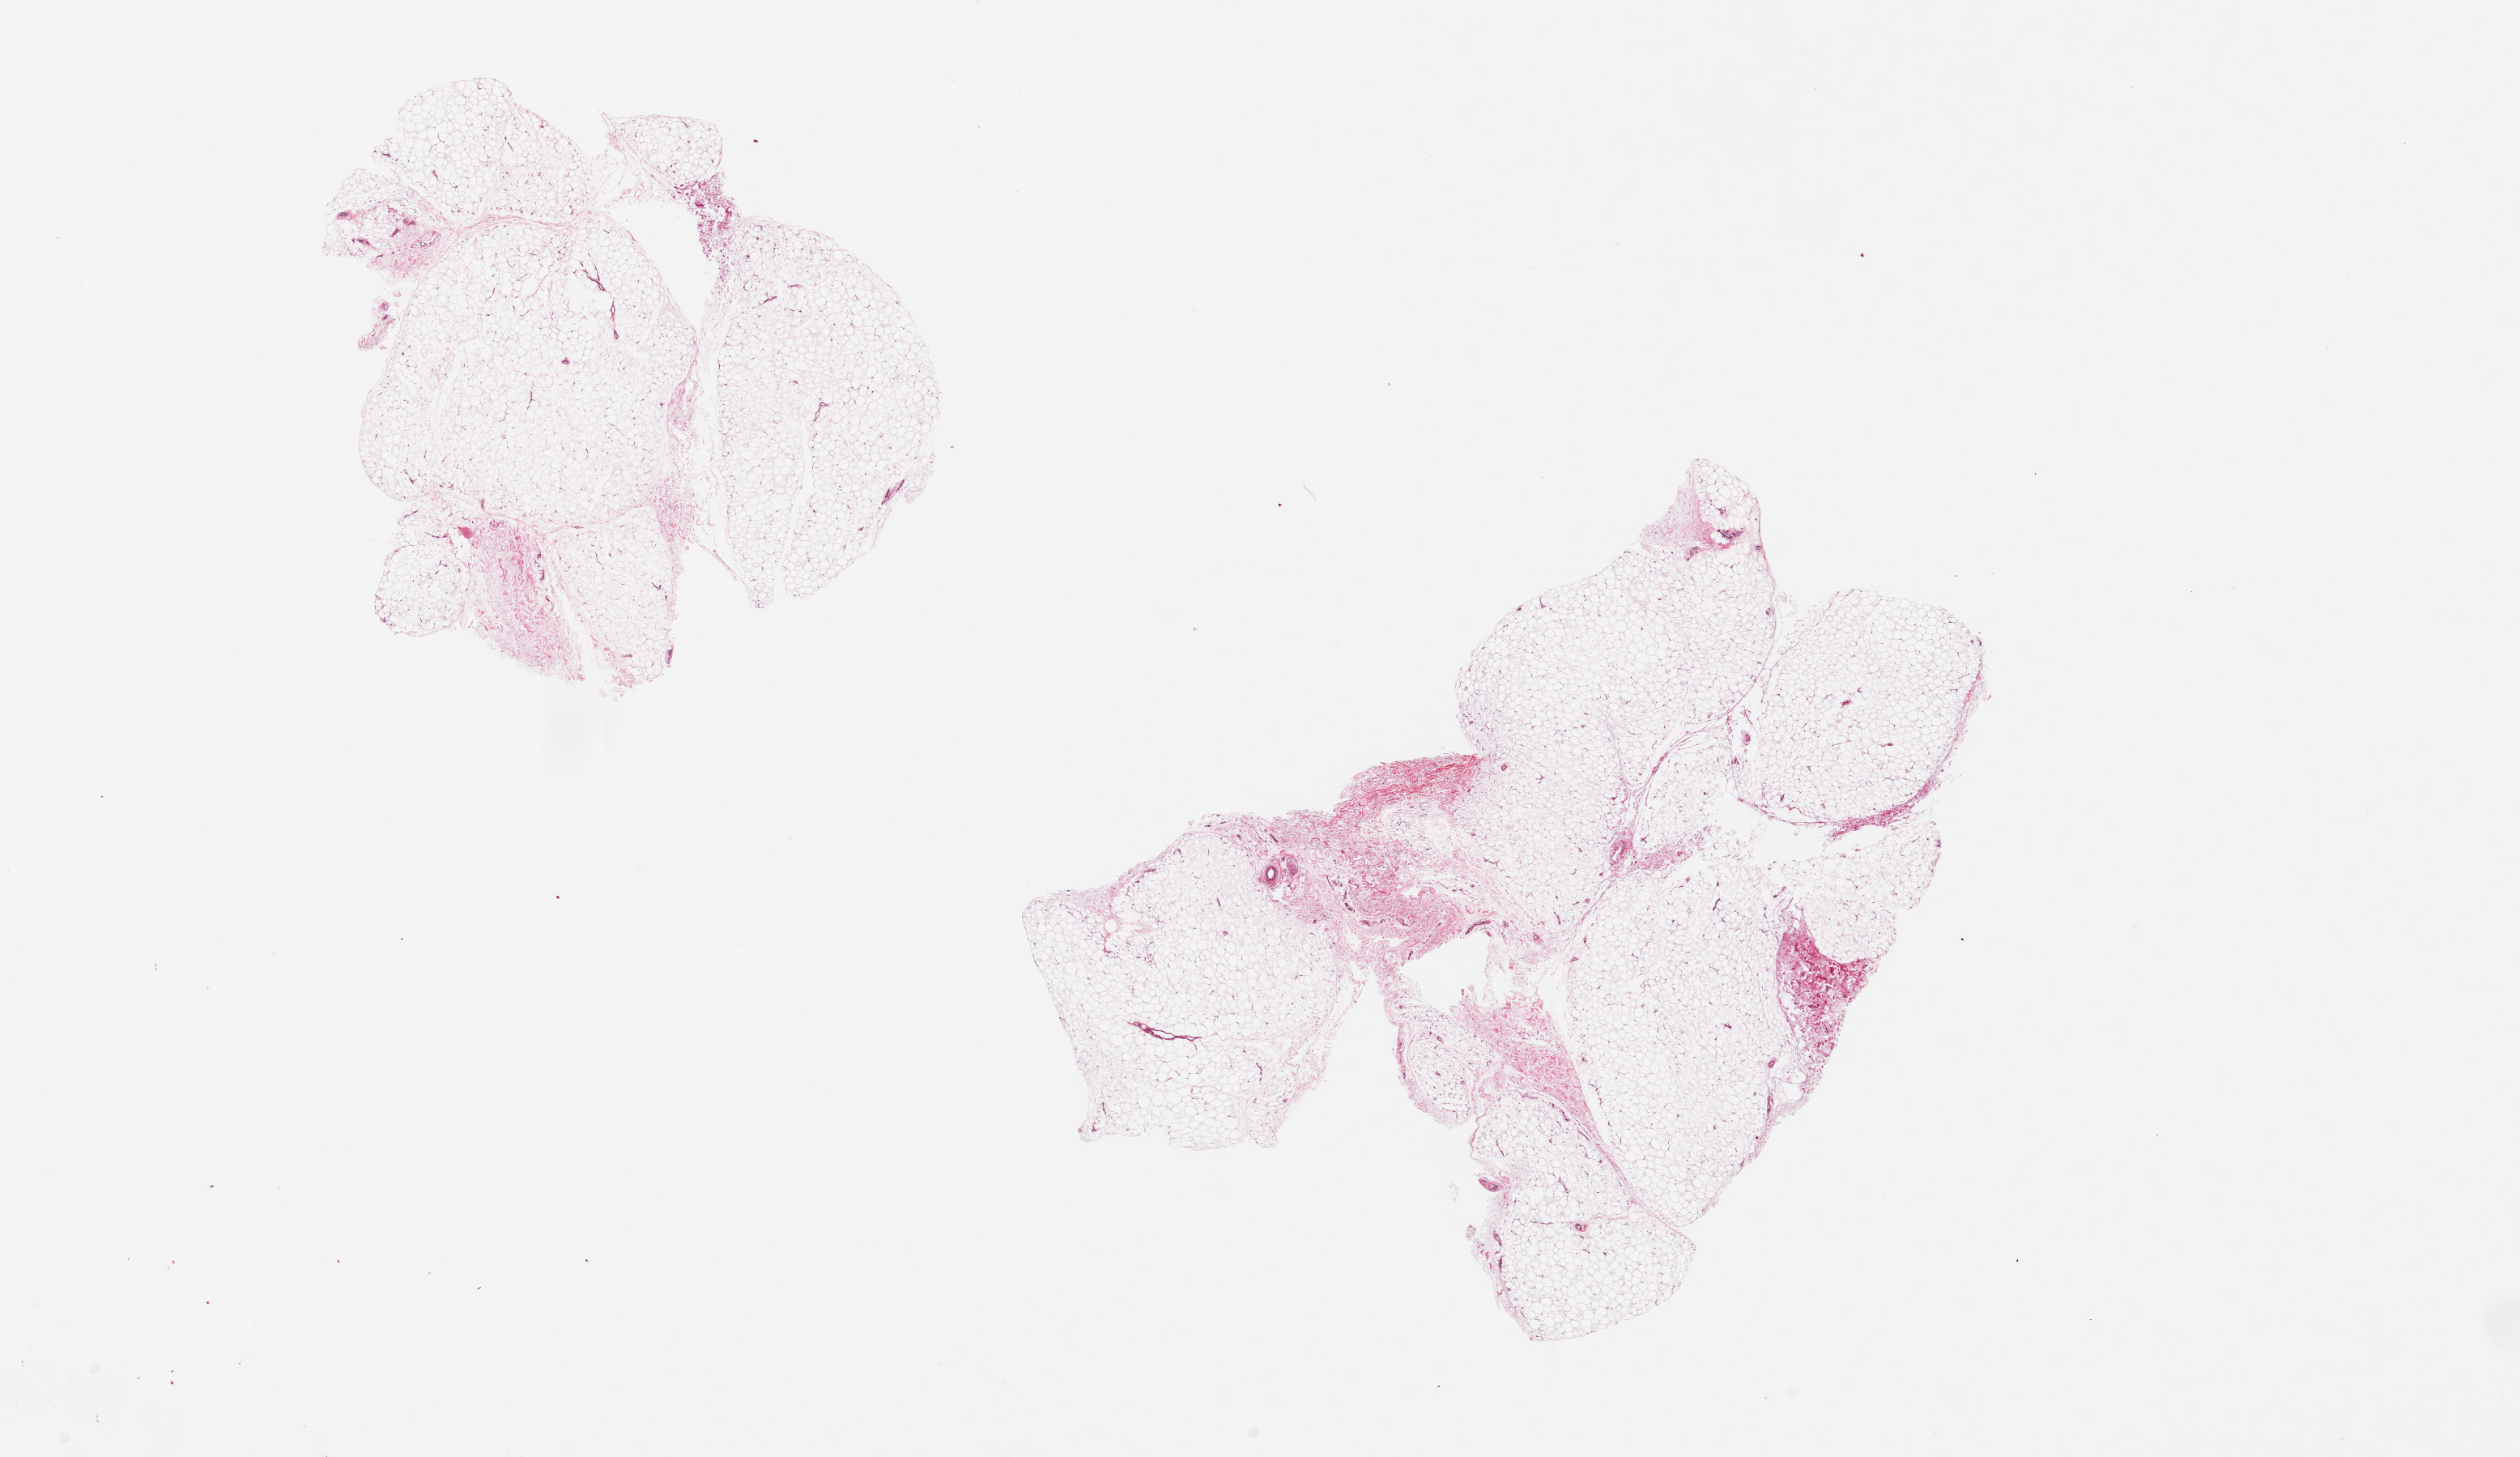
Whole-slide image, H&E stain, shown as a low-resolution overview of the whole scanned area (about 24.6 x 14.2 mm), PAXgene-fixed, paraffin-embedded tissue, section of adipose tissue (target tissue), donor tissue sample. Male donor.
Reviewer comment on this tissue sample: 2 pieces, 6x6 & 9x7mm; well fixed, no artifacts.